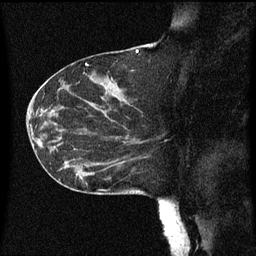
Breast MRI (dynamic contrast-enhanced), one sagittal slice; slice 29 of 60 in the series (ordered by position); dynamic contrast-enhanced series, image 2 of 3 at this slice position (ordered by acquisition); 1.5 T; TE 4.2 ms, TR 8 ms; 2 mm slice thickness; 256 × 256 image matrix, field of view 200 × 200 mm. Patient: female, 55 years.
Structures marked on this image (semi-automatically segmented with operator editing):
- analysis volume of interest (the breast-tissue region the enhancement analysis was run in; not a lesion): bounding box [x1, y1, x2, y2] px = [46, 124, 151, 183]
- tumour enhancement mask (voxels above the 70 % enhancement threshold inside the analysis volume of interest): [80, 138, 147, 179]